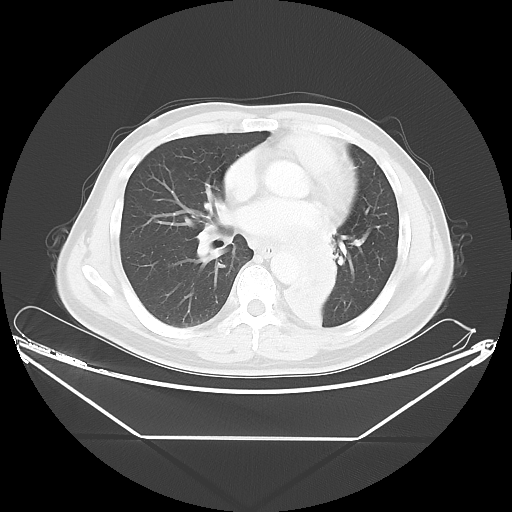
Chest CT, one axial slice. Lung window (W 1500 / L -600 HU). 512 × 512 image matrix, field of view 438 × 438 mm. Male patient, age 58 years. From the clinical record (not read from this slice): clinical TNM (as recorded): T3 N3 M0.
Structures marked on this image (bounding box drawn by a radiologist):
- lung tumour (recorded histology: squamous cell carcinoma): bounding box [x1, y1, x2, y2] px = [267, 209, 349, 333]